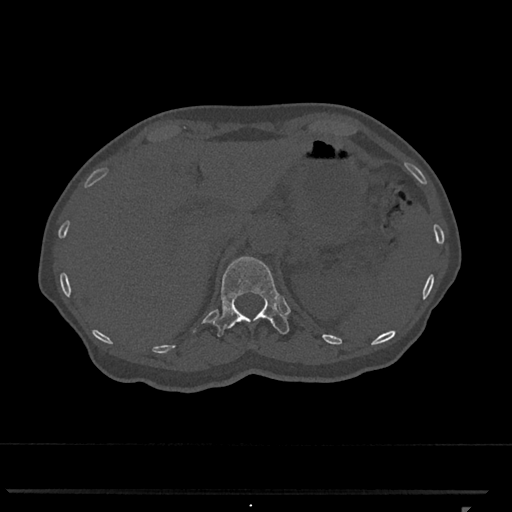
CT including the spine, one axial slice; position 467 of 793 along the scan axis; reconstruction kernel Br40s/3; 120 kVp; bone window (W 1800 / L 400 HU); 512 × 512 image matrix. Female patient, age 62 years. From the clinical record (not read from this slice): primary cancer: renal.
Structures marked on this image (semi-automatically segmented with operator editing):
- T12 vertebra: bounding box [x1, y1, x2, y2] px = [212, 256, 289, 337]